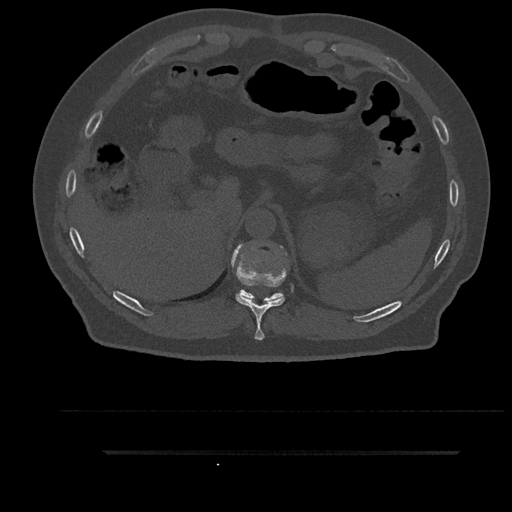
CT including the spine, one axial slice; slice 342 of 797 in the series (ordered by position); reconstruction kernel Br40s/3; 120 kVp; bone window (W 1800 / L 400 HU); 0.5 mm slice thickness; 512 × 512 image matrix. Male patient, age 63 years. From the clinical record (not read from this slice): primary cancer: renal.
Outlined on this slice (semi-automatic segmentation, software-assisted and operator-edited):
- T10 vertebra: bounding box [x1, y1, x2, y2] px = [231, 244, 287, 340]
- T11 vertebra: [237, 290, 284, 302]